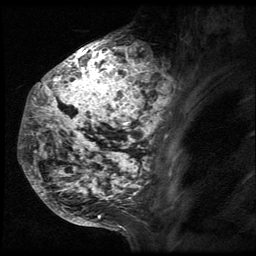
Breast MRI (dynamic contrast-enhanced), one sagittal slice. 3 images stored at this slice position (order not interpretable as contrast timing). 1.5 T. TE 4.2 ms, TR 9 ms. 256 × 256 image matrix, field of view 180 × 180 mm. Patient: female, 50 years. From the clinical record (not read from this slice): setting: breast cancer imaged before/during neoadjuvant chemotherapy; receptor status: triple-negative.
Annotated regions visible in this slice (semi-automatically segmented with operator editing):
- analysis volume of interest (the breast-tissue region the enhancement analysis was run in; not a lesion): bounding box [x1, y1, x2, y2] px = [24, 39, 181, 212]
- tumour enhancement mask (voxels above the 140 % enhancement threshold inside the analysis volume of interest): [24, 39, 180, 210]